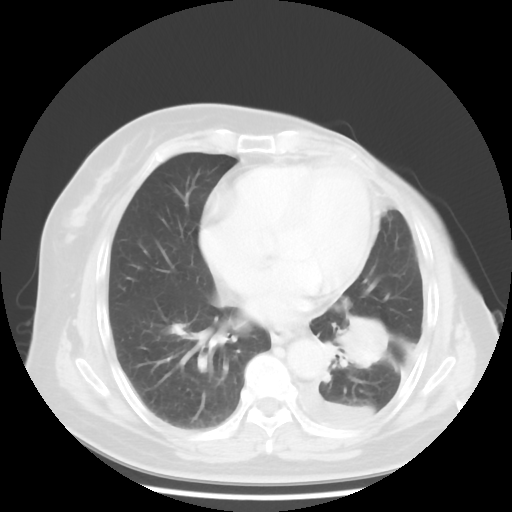
Chest CT, one axial slice; position 18 of 48 along the scan axis; lung window (W 1500 / L -600 HU); 5 mm slice thickness; 512 × 512 image matrix. Patient: female, 63 years. From the clinical record (not read from this slice): clinical TNM (as recorded): T2 N0 M1.
Structures marked on this image (rectangle marked by the reading radiologist):
- lung tumour (recorded histology: adenocarcinoma): box from (x=325, y=307) to (x=392, y=374) px